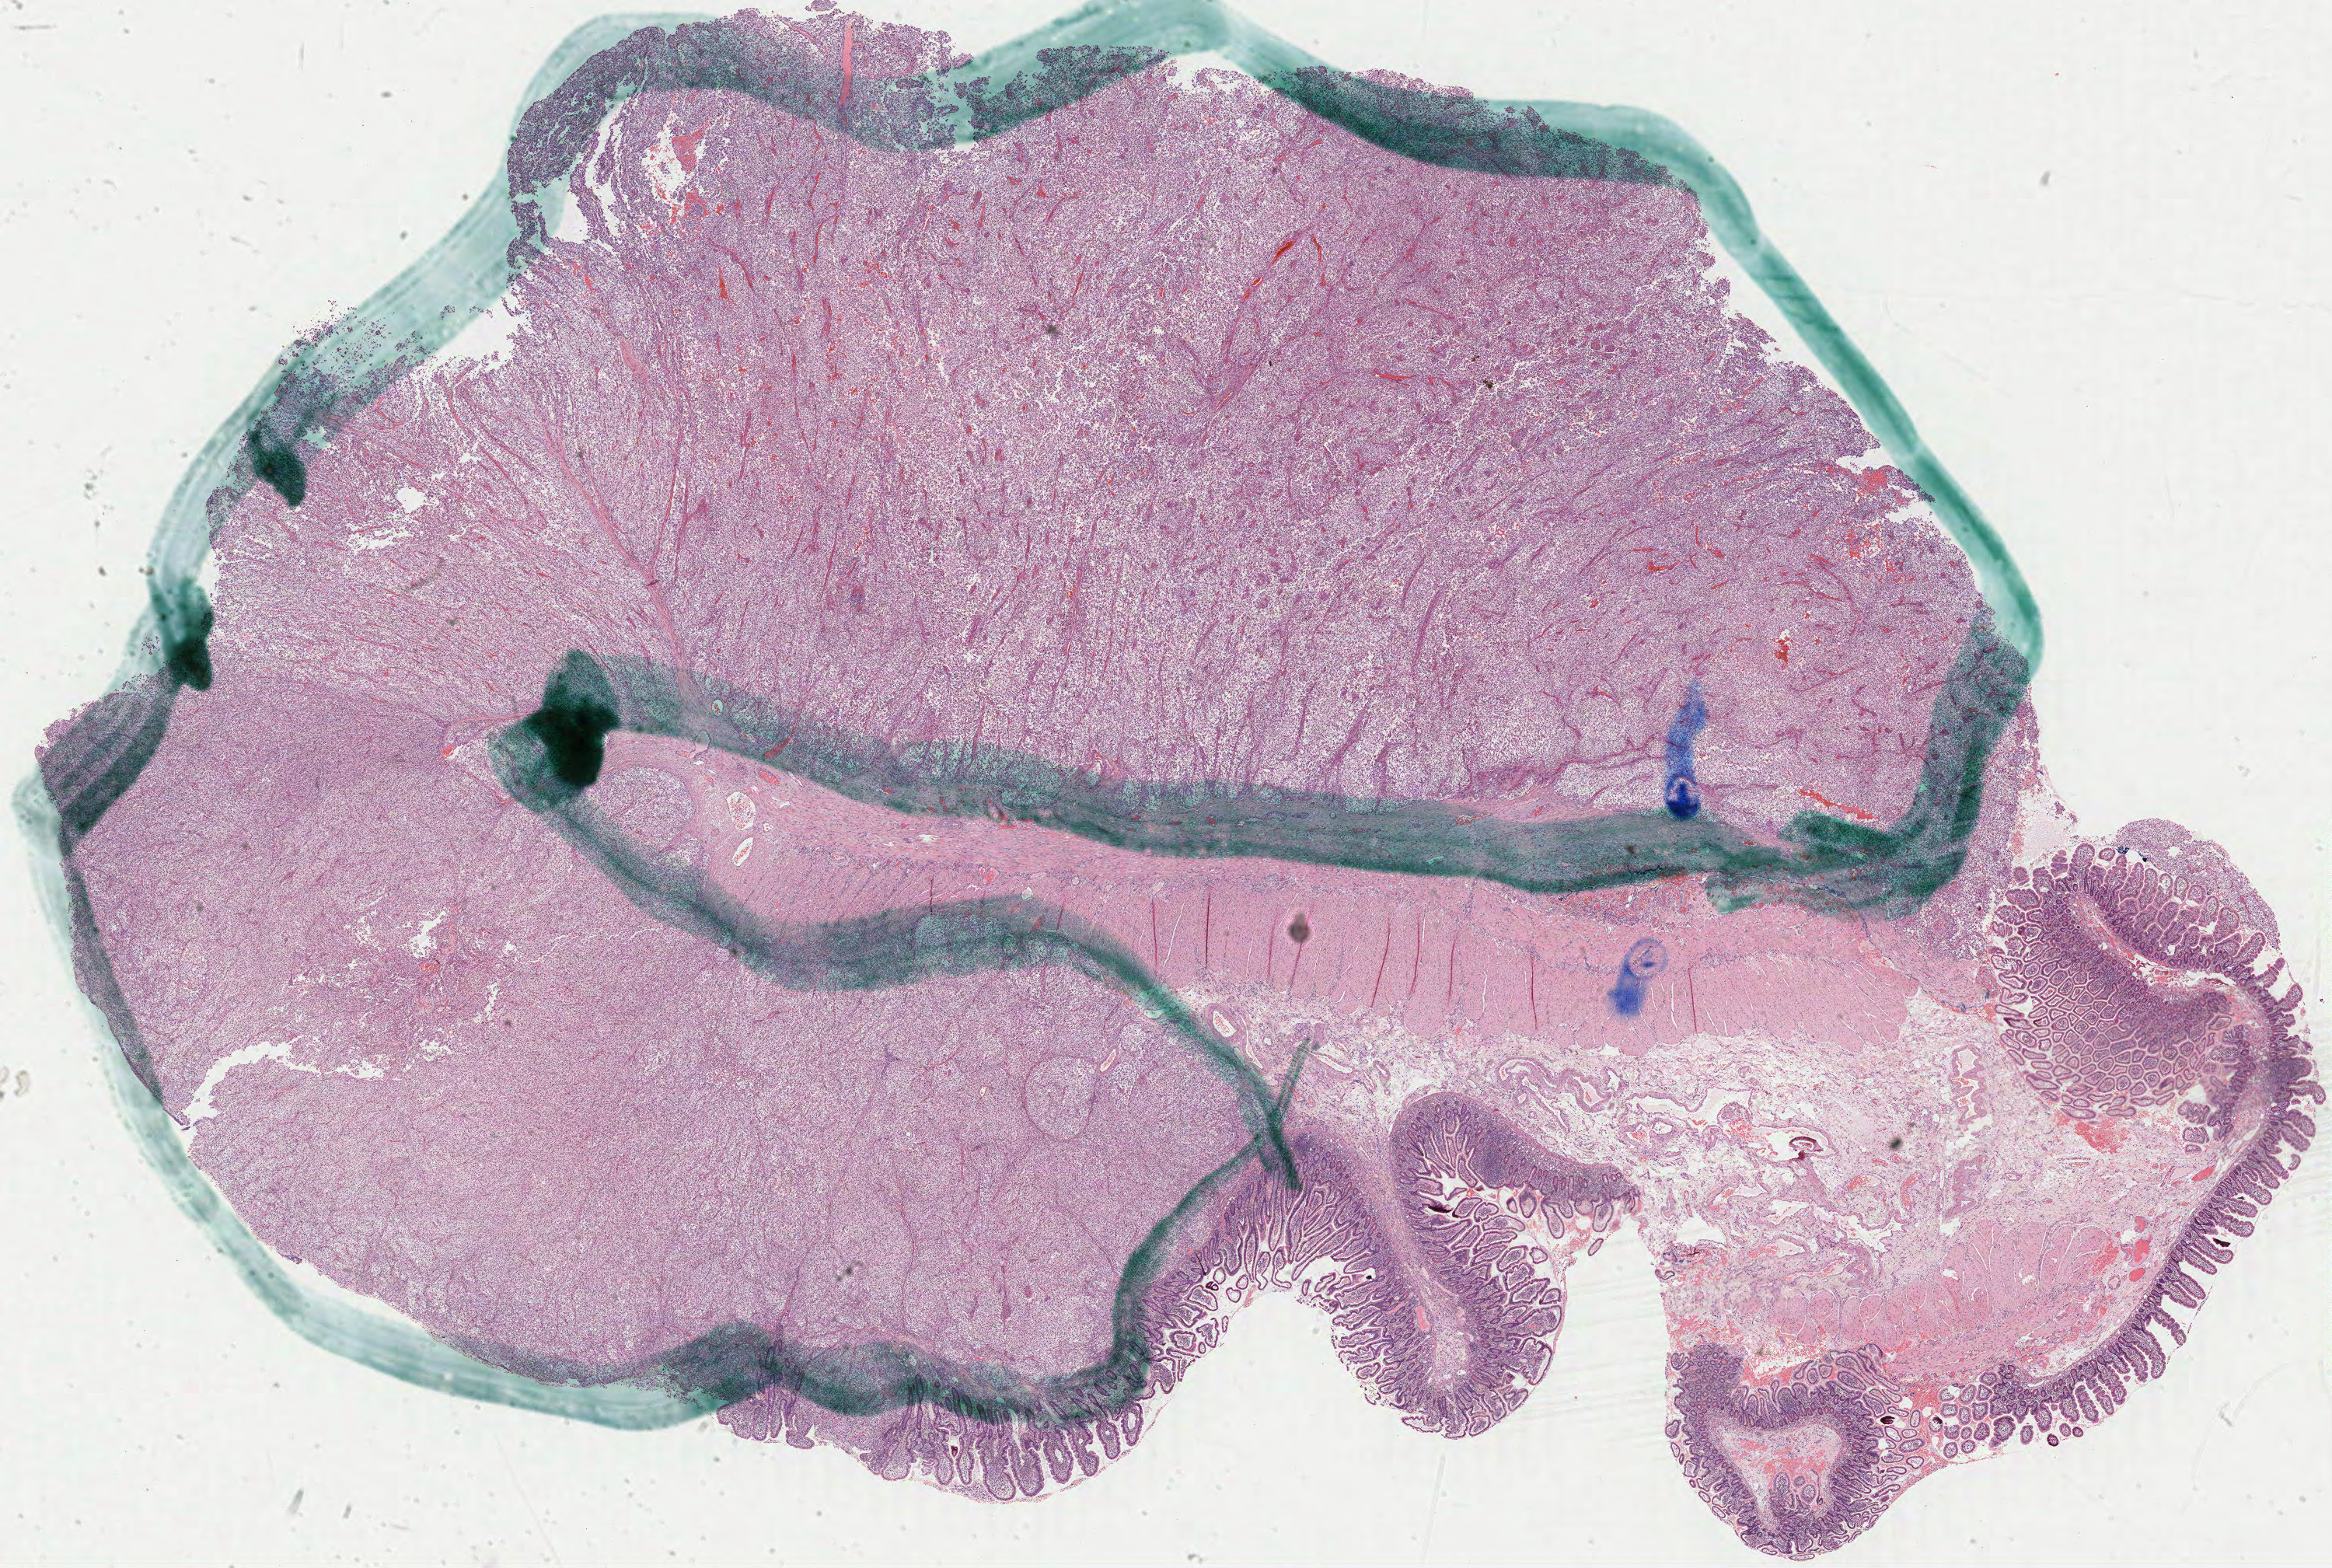
H&E whole-slide image — shown as a low-resolution overview of the whole scanned area (about 24.1 x 16.2 mm, acquisition: 40x scan). FFPE section. Metastatic tumour sample, sampled site not recorded. Female, age 54 years at initial diagnosis.
This section: metastatic tumour tissue. Patient diagnosis: Malignant melanoma, NOS.